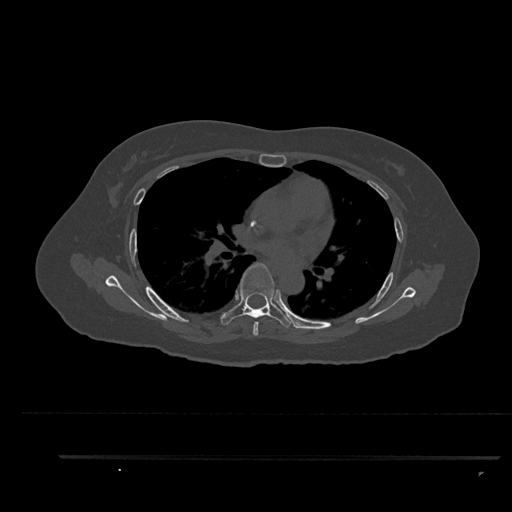
CT including the spine, one axial slice; slice 568 of 797 in the series (ordered by position); 120 kVp; bone window (W 1800 / L 400 HU); 0.5 mm slice thickness; 512 × 512 image matrix. Female patient, age 44 years. Case-level facts recorded for this patient, not image findings: primary cancer: renal; vertebrae with lytic lesions (as recorded): L1.
Outlined on this slice (semi-automatic segmentation, software-assisted and operator-edited):
- T5 vertebra: bounding box <253,322,259,336> (left, top, right, bottom; pixels)
- T6 vertebra: <220,263,293,328>